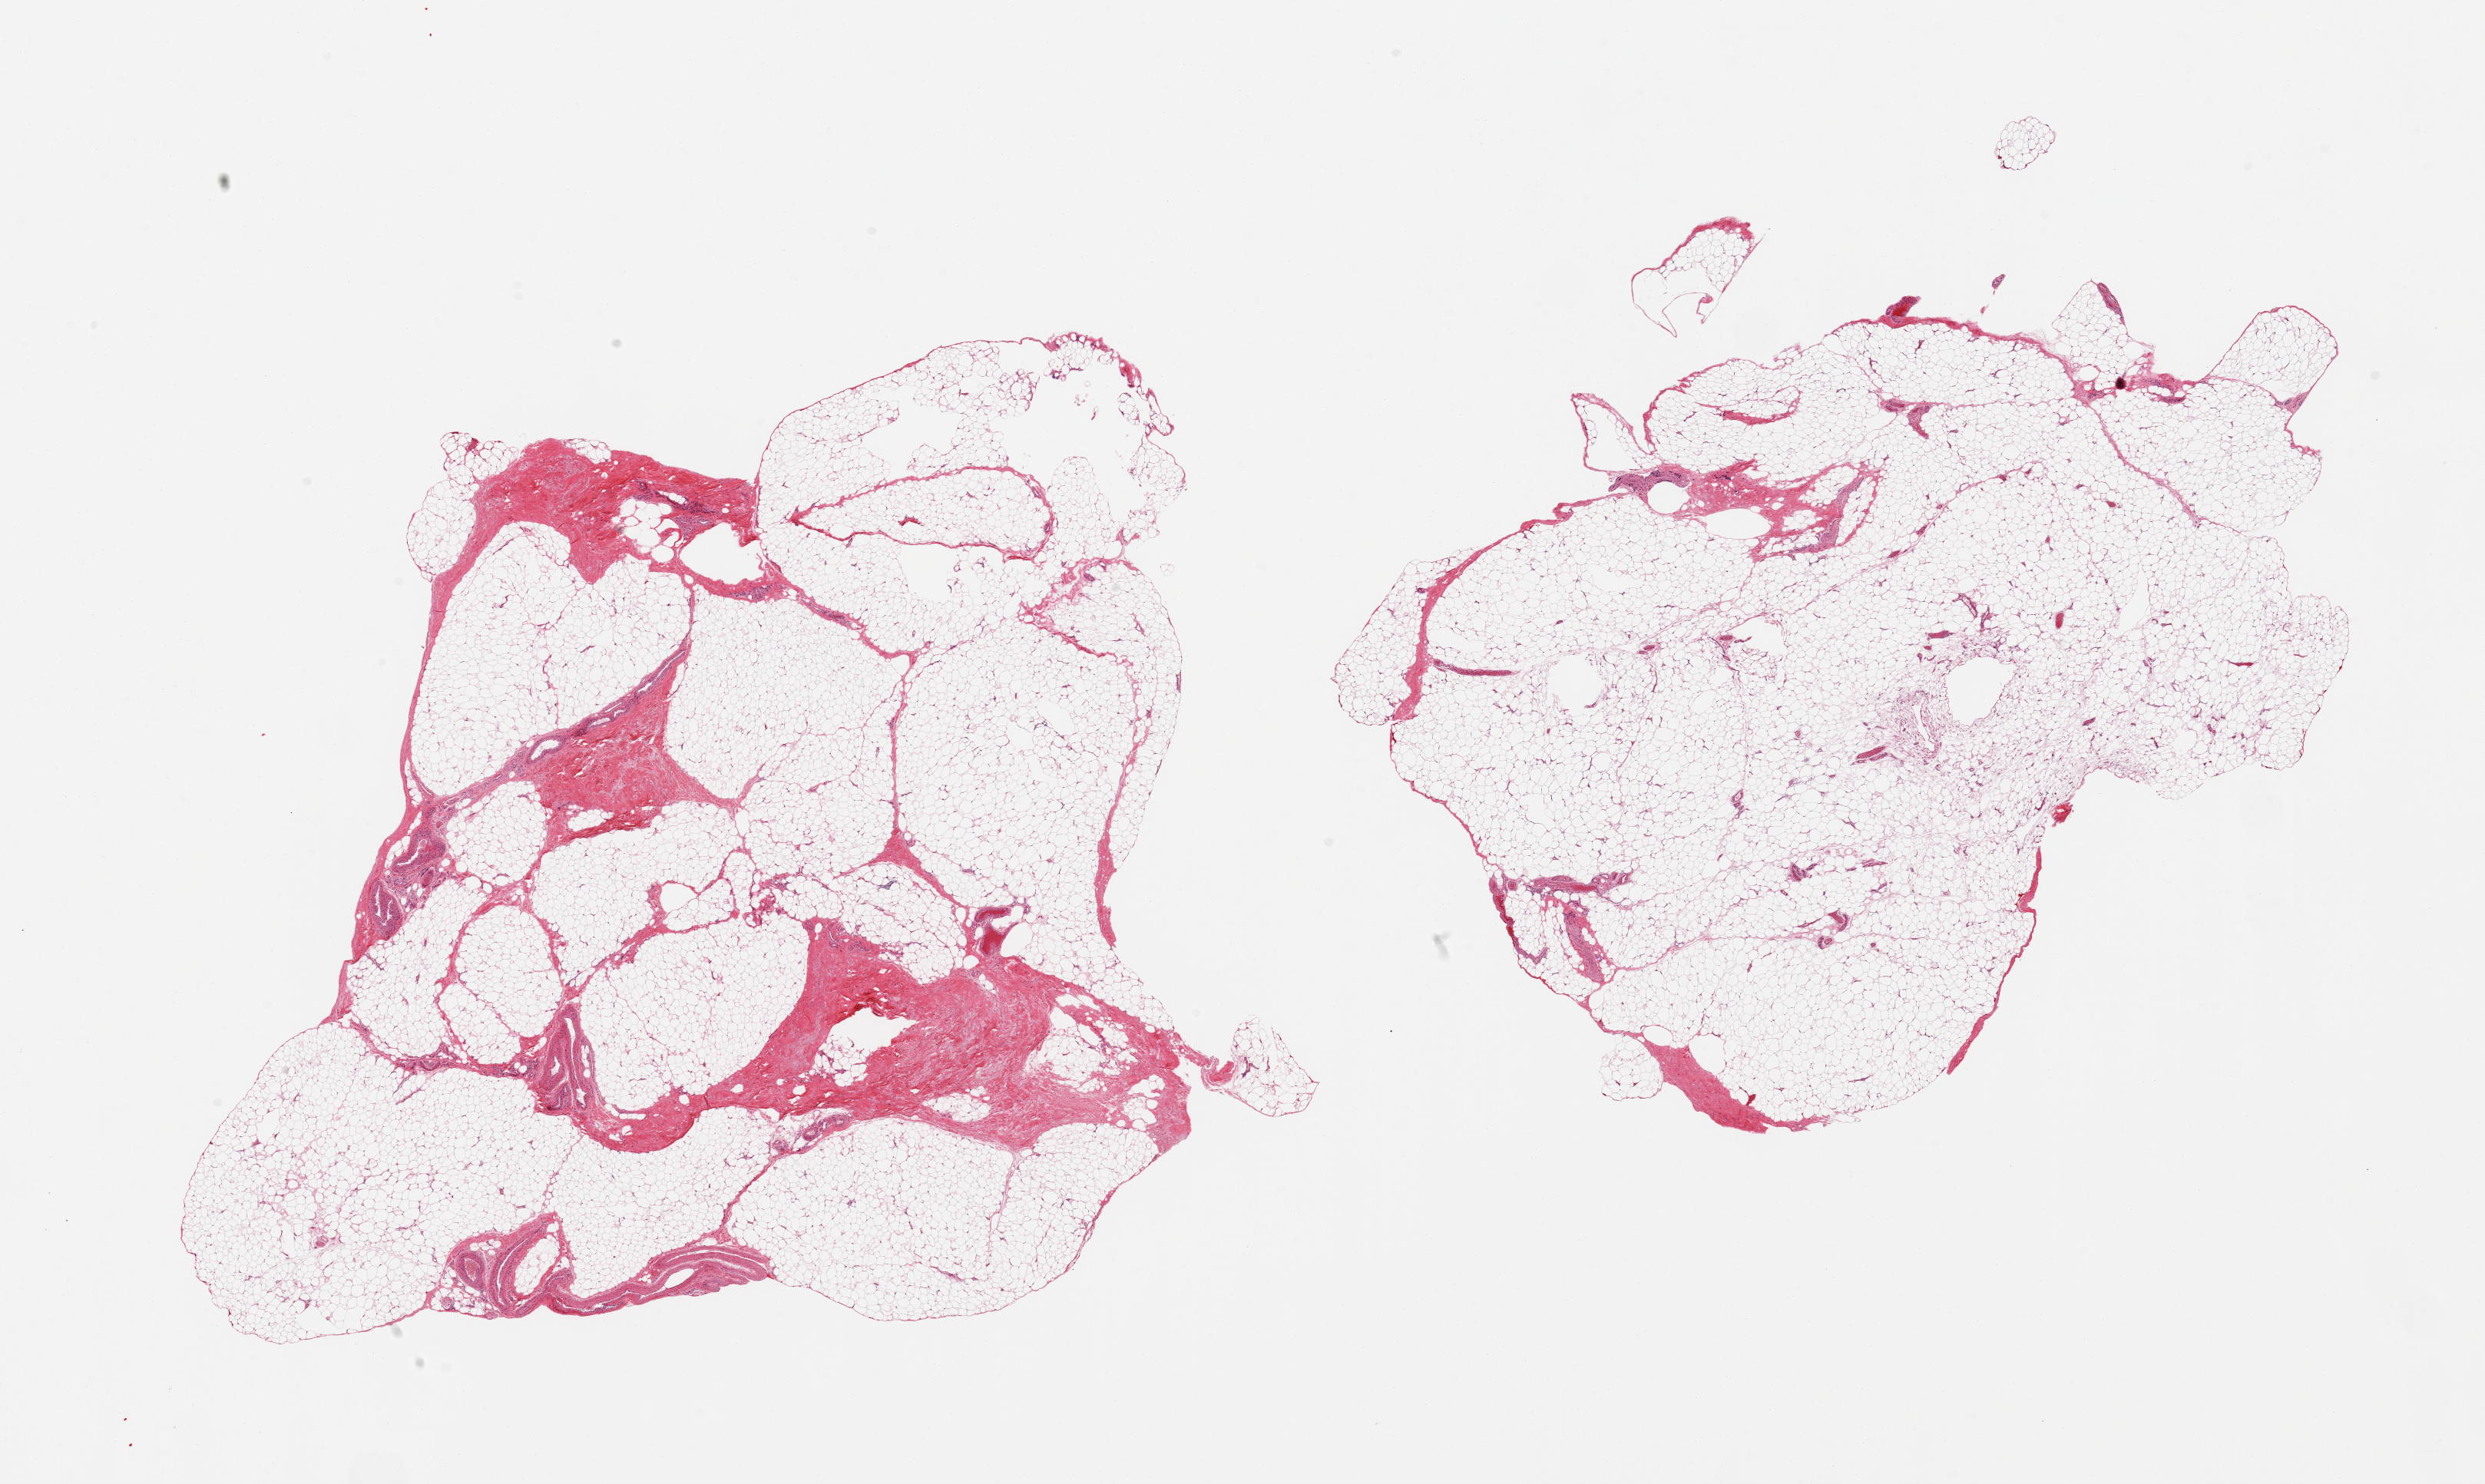
Whole-slide image, H&E stain, whole scanned area (about 25.6 x 15.3 mm) shown as a low-resolution overview; PAXgene-fixed paraffin-embedded (PFPE) section; section of adipose tissue (target tissue); tissue donor sample. Donor: male.
• reviewer comment on this tissue sample: 2 pieces, ~10-20% fascia/vascular elements